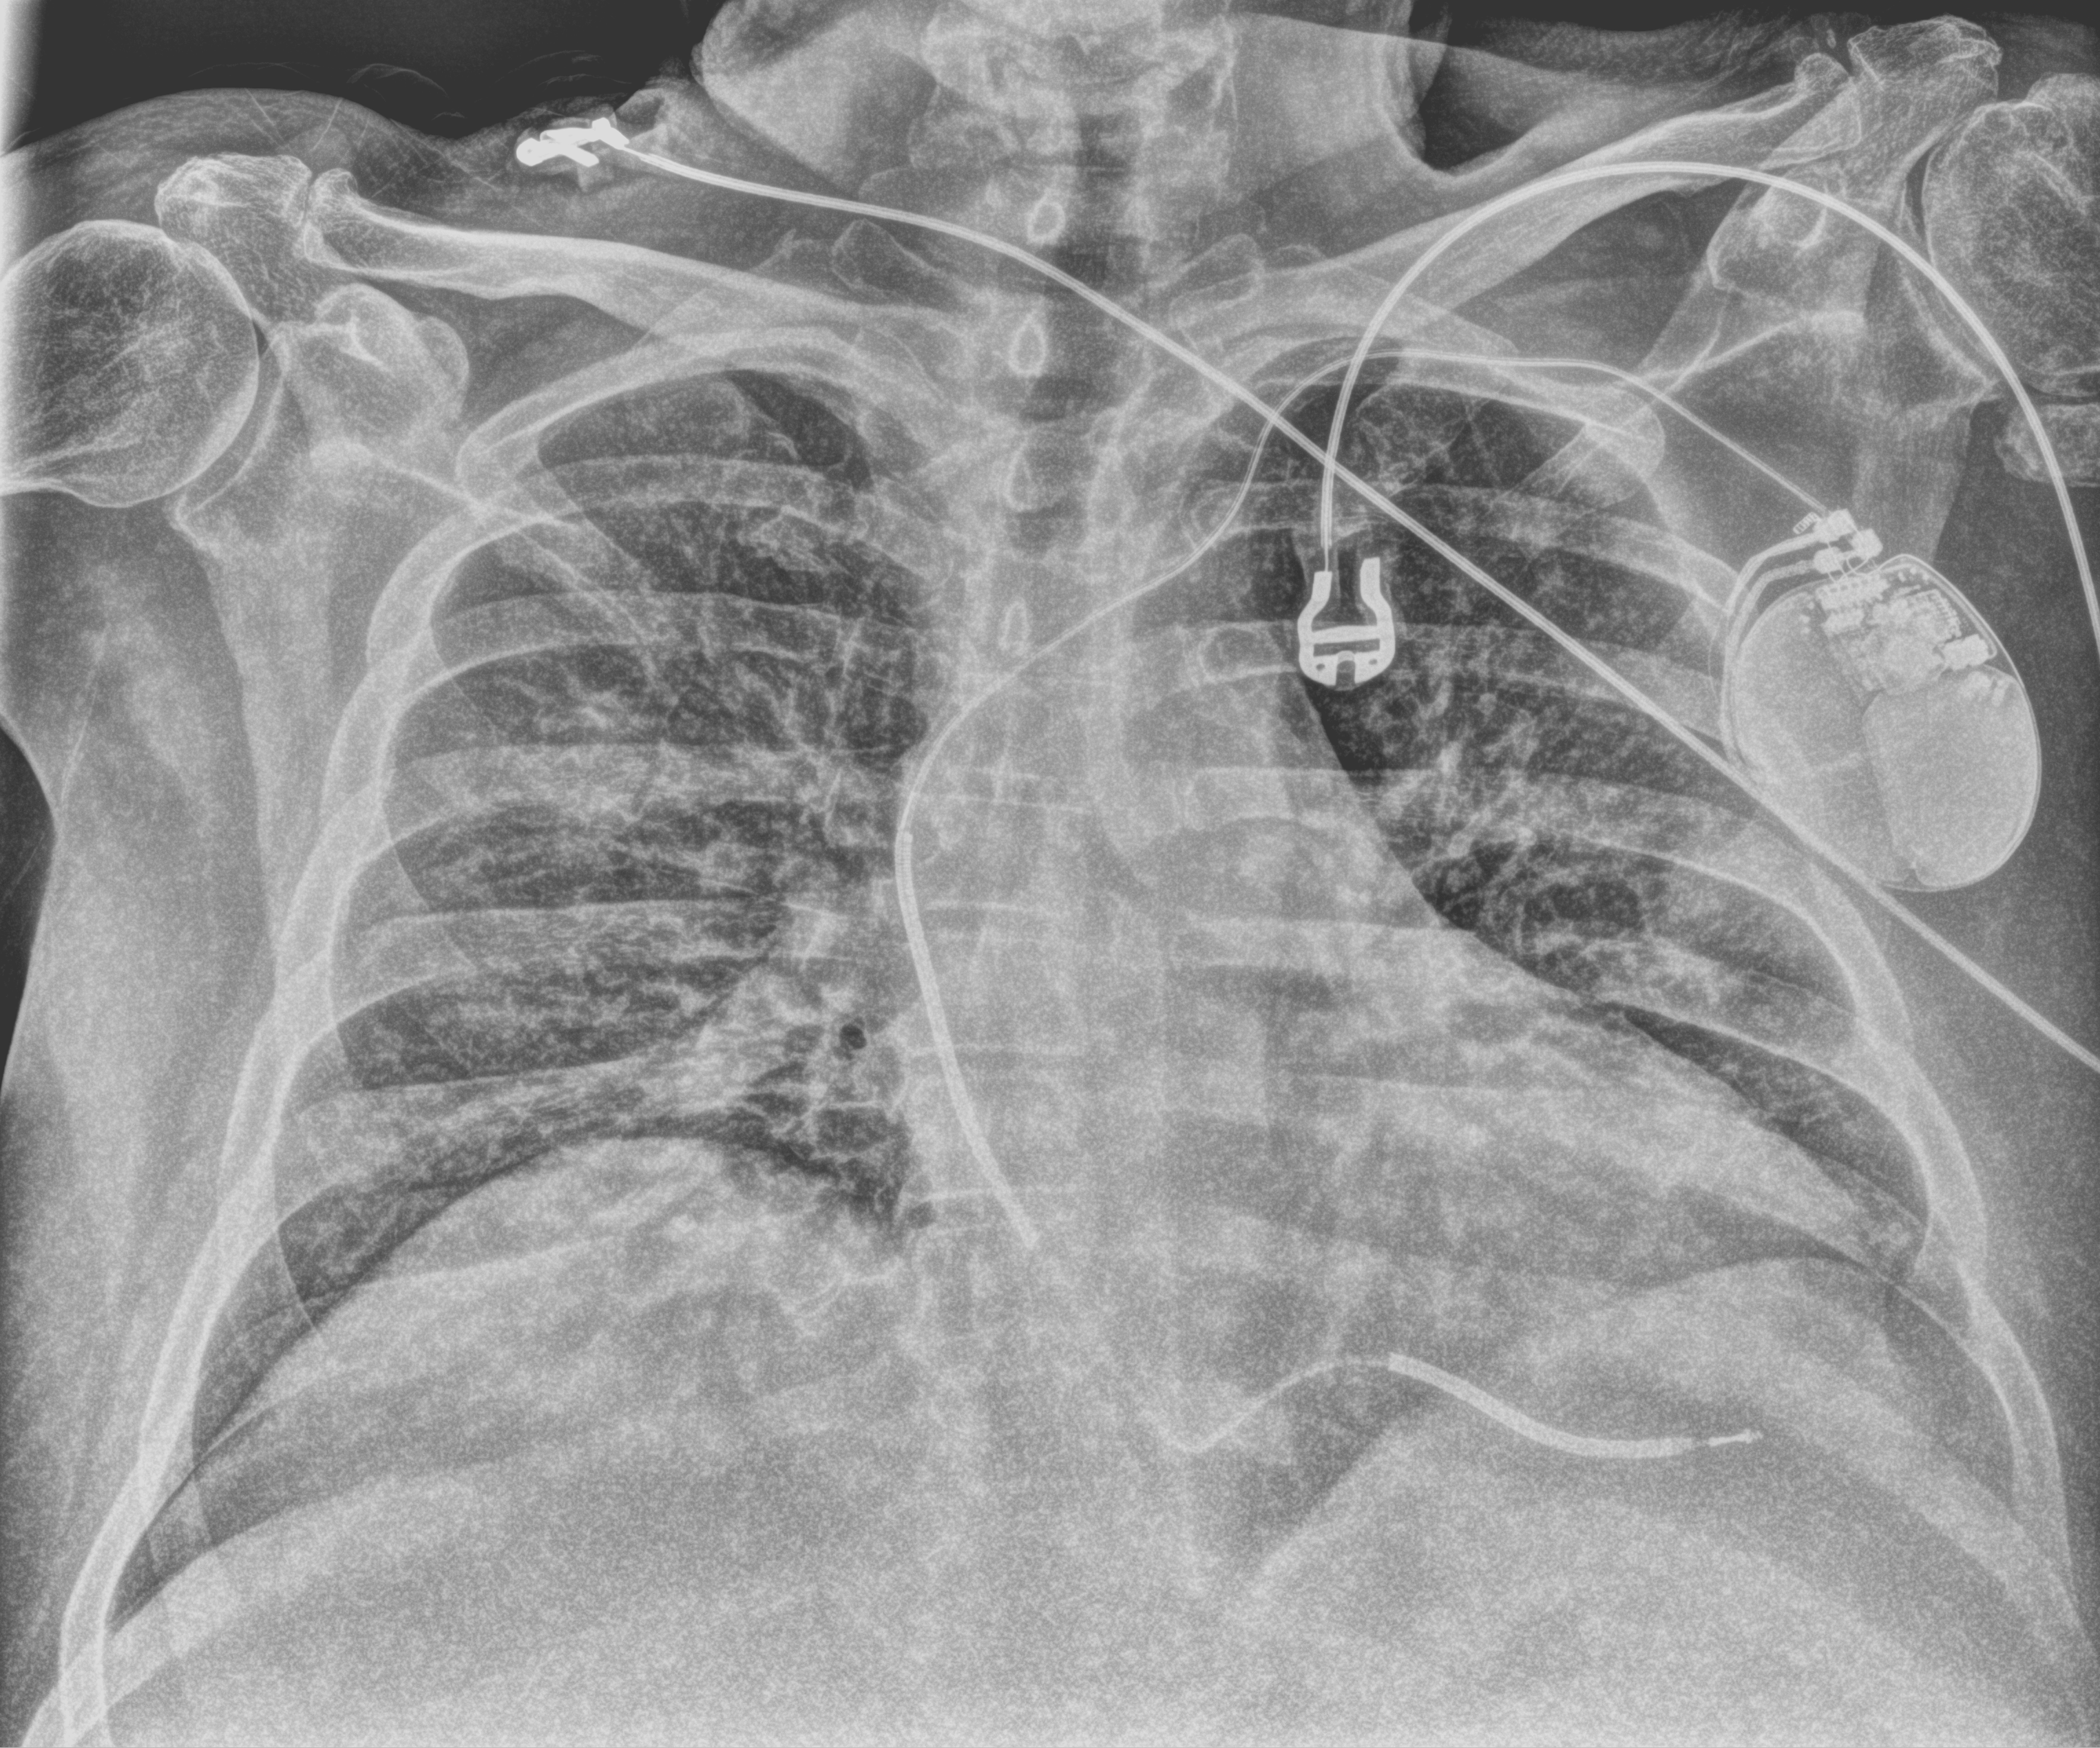
Chest X-ray (portable); anteroposterior (AP) projection. Patient hospitalised with COVID-19; male, aged 60–74 years.
Admission-level facts for this patient (not findings on this image; timing relative to this image not recorded):
- mechanically ventilated during this hospital stay: no
- admitted to intensive care during this hospital stay: no